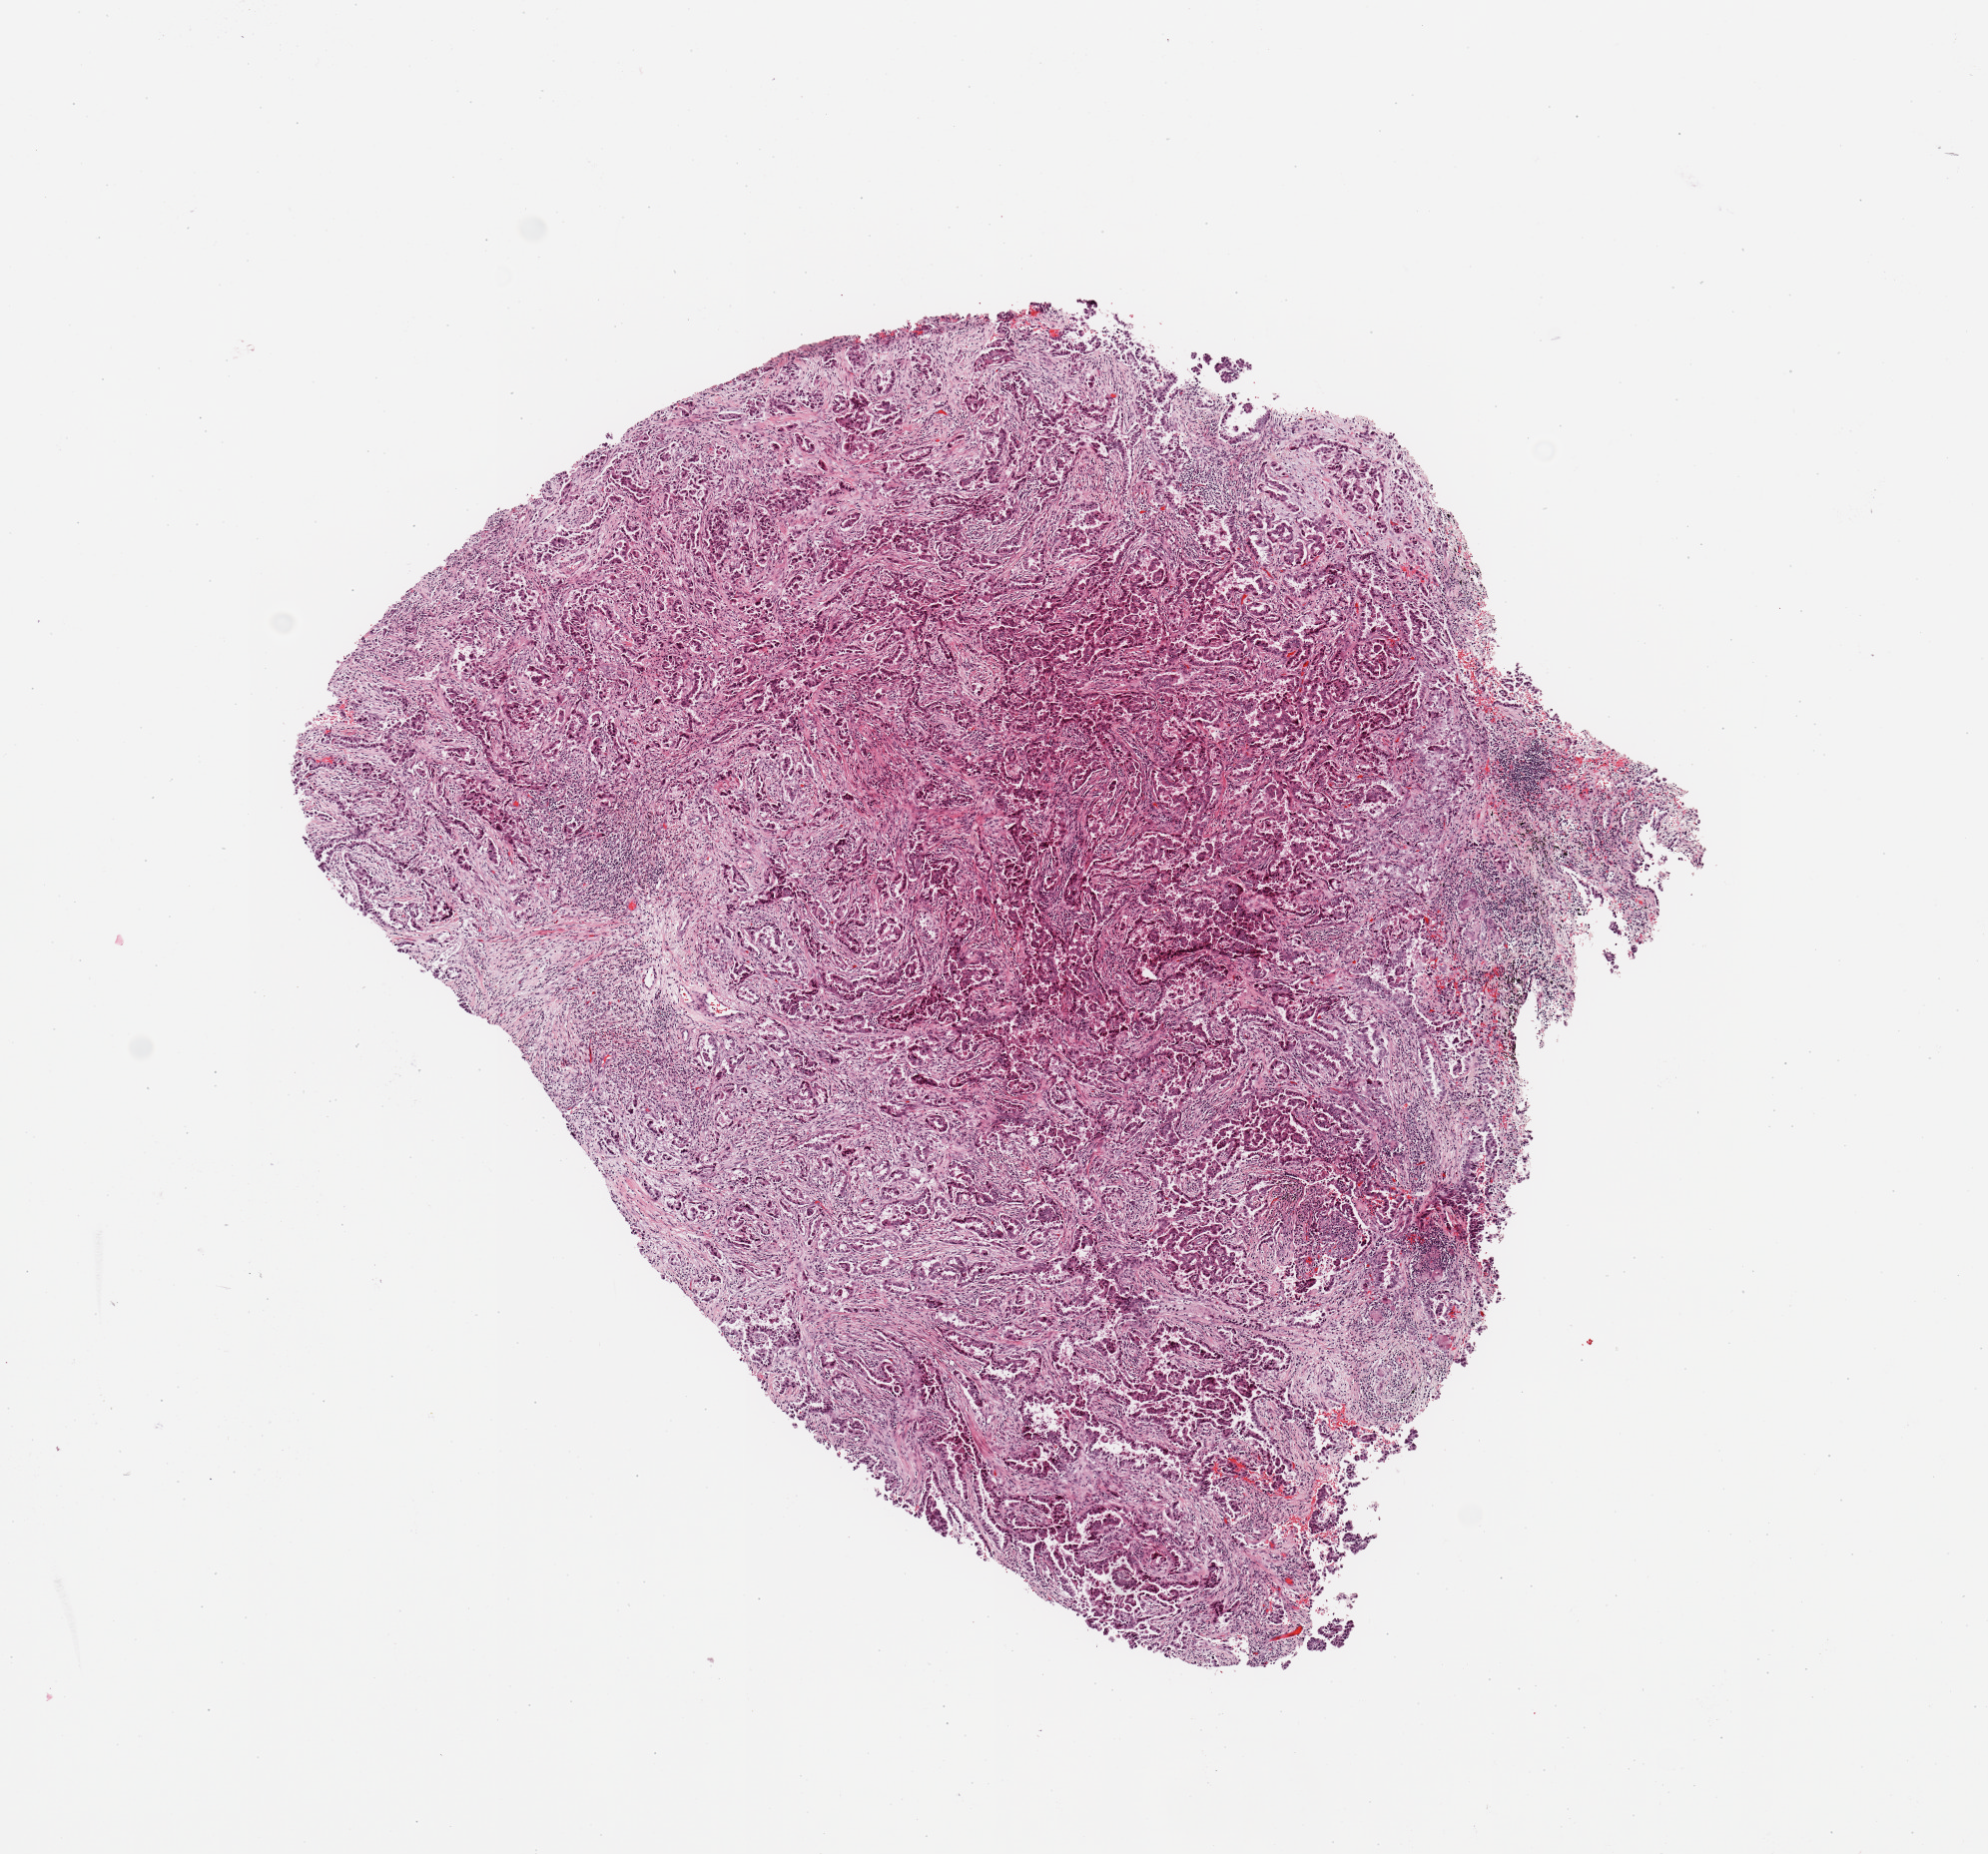
Hematoxylin and eosin (H&E) stained whole-slide image — low-resolution overview of the scanned area, about 7.9 x 7.3 mm (acquisition: 20x scan). Tumour tissue sample, sampled site: lung. Patient: female, age 72 years. Histologic grade: G2 (moderately differentiated). Pathologist review of this section (percent, as recorded): tumour nuclei 65%, necrosis 3%.
Histologic diagnosis: Adenocarcinoma, NOS. AJCC pathologic stage: IA3.